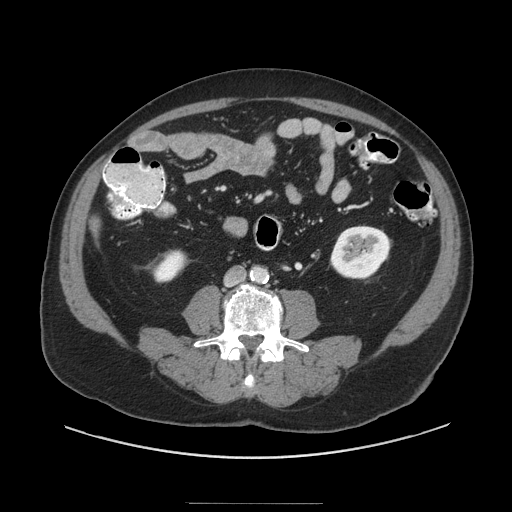
Contrast-enhanced abdominal CT (liver protocol), one axial slice. Slice 13 of 91 in the series (ordered by position). Reconstruction kernel STANDARD. 140 kVp. Soft-tissue window (W 400 / L 40 HU). 2.5 mm slice thickness. 512 × 512 image matrix. Case-level facts recorded for this patient, not image findings: diagnosis: hepatocellular carcinoma (patient treated with transarterial chemoembolisation; whether this scan precedes or follows treatment is not stated here); TNM stage (as recorded): Stage-I; Child-Pugh class: A; tumour differentiation: well differentiated; tumour nodularity: uninodular.
Structures marked on this image (semi-automatic segmentation, software-assisted and operator-edited):
- liver parenchyma outside the tumour (the mass and vessels are separate outlines, so this box may not span the whole liver): bounding box (x1, y1, x2, y2) in pixels: (92, 218, 100, 232)